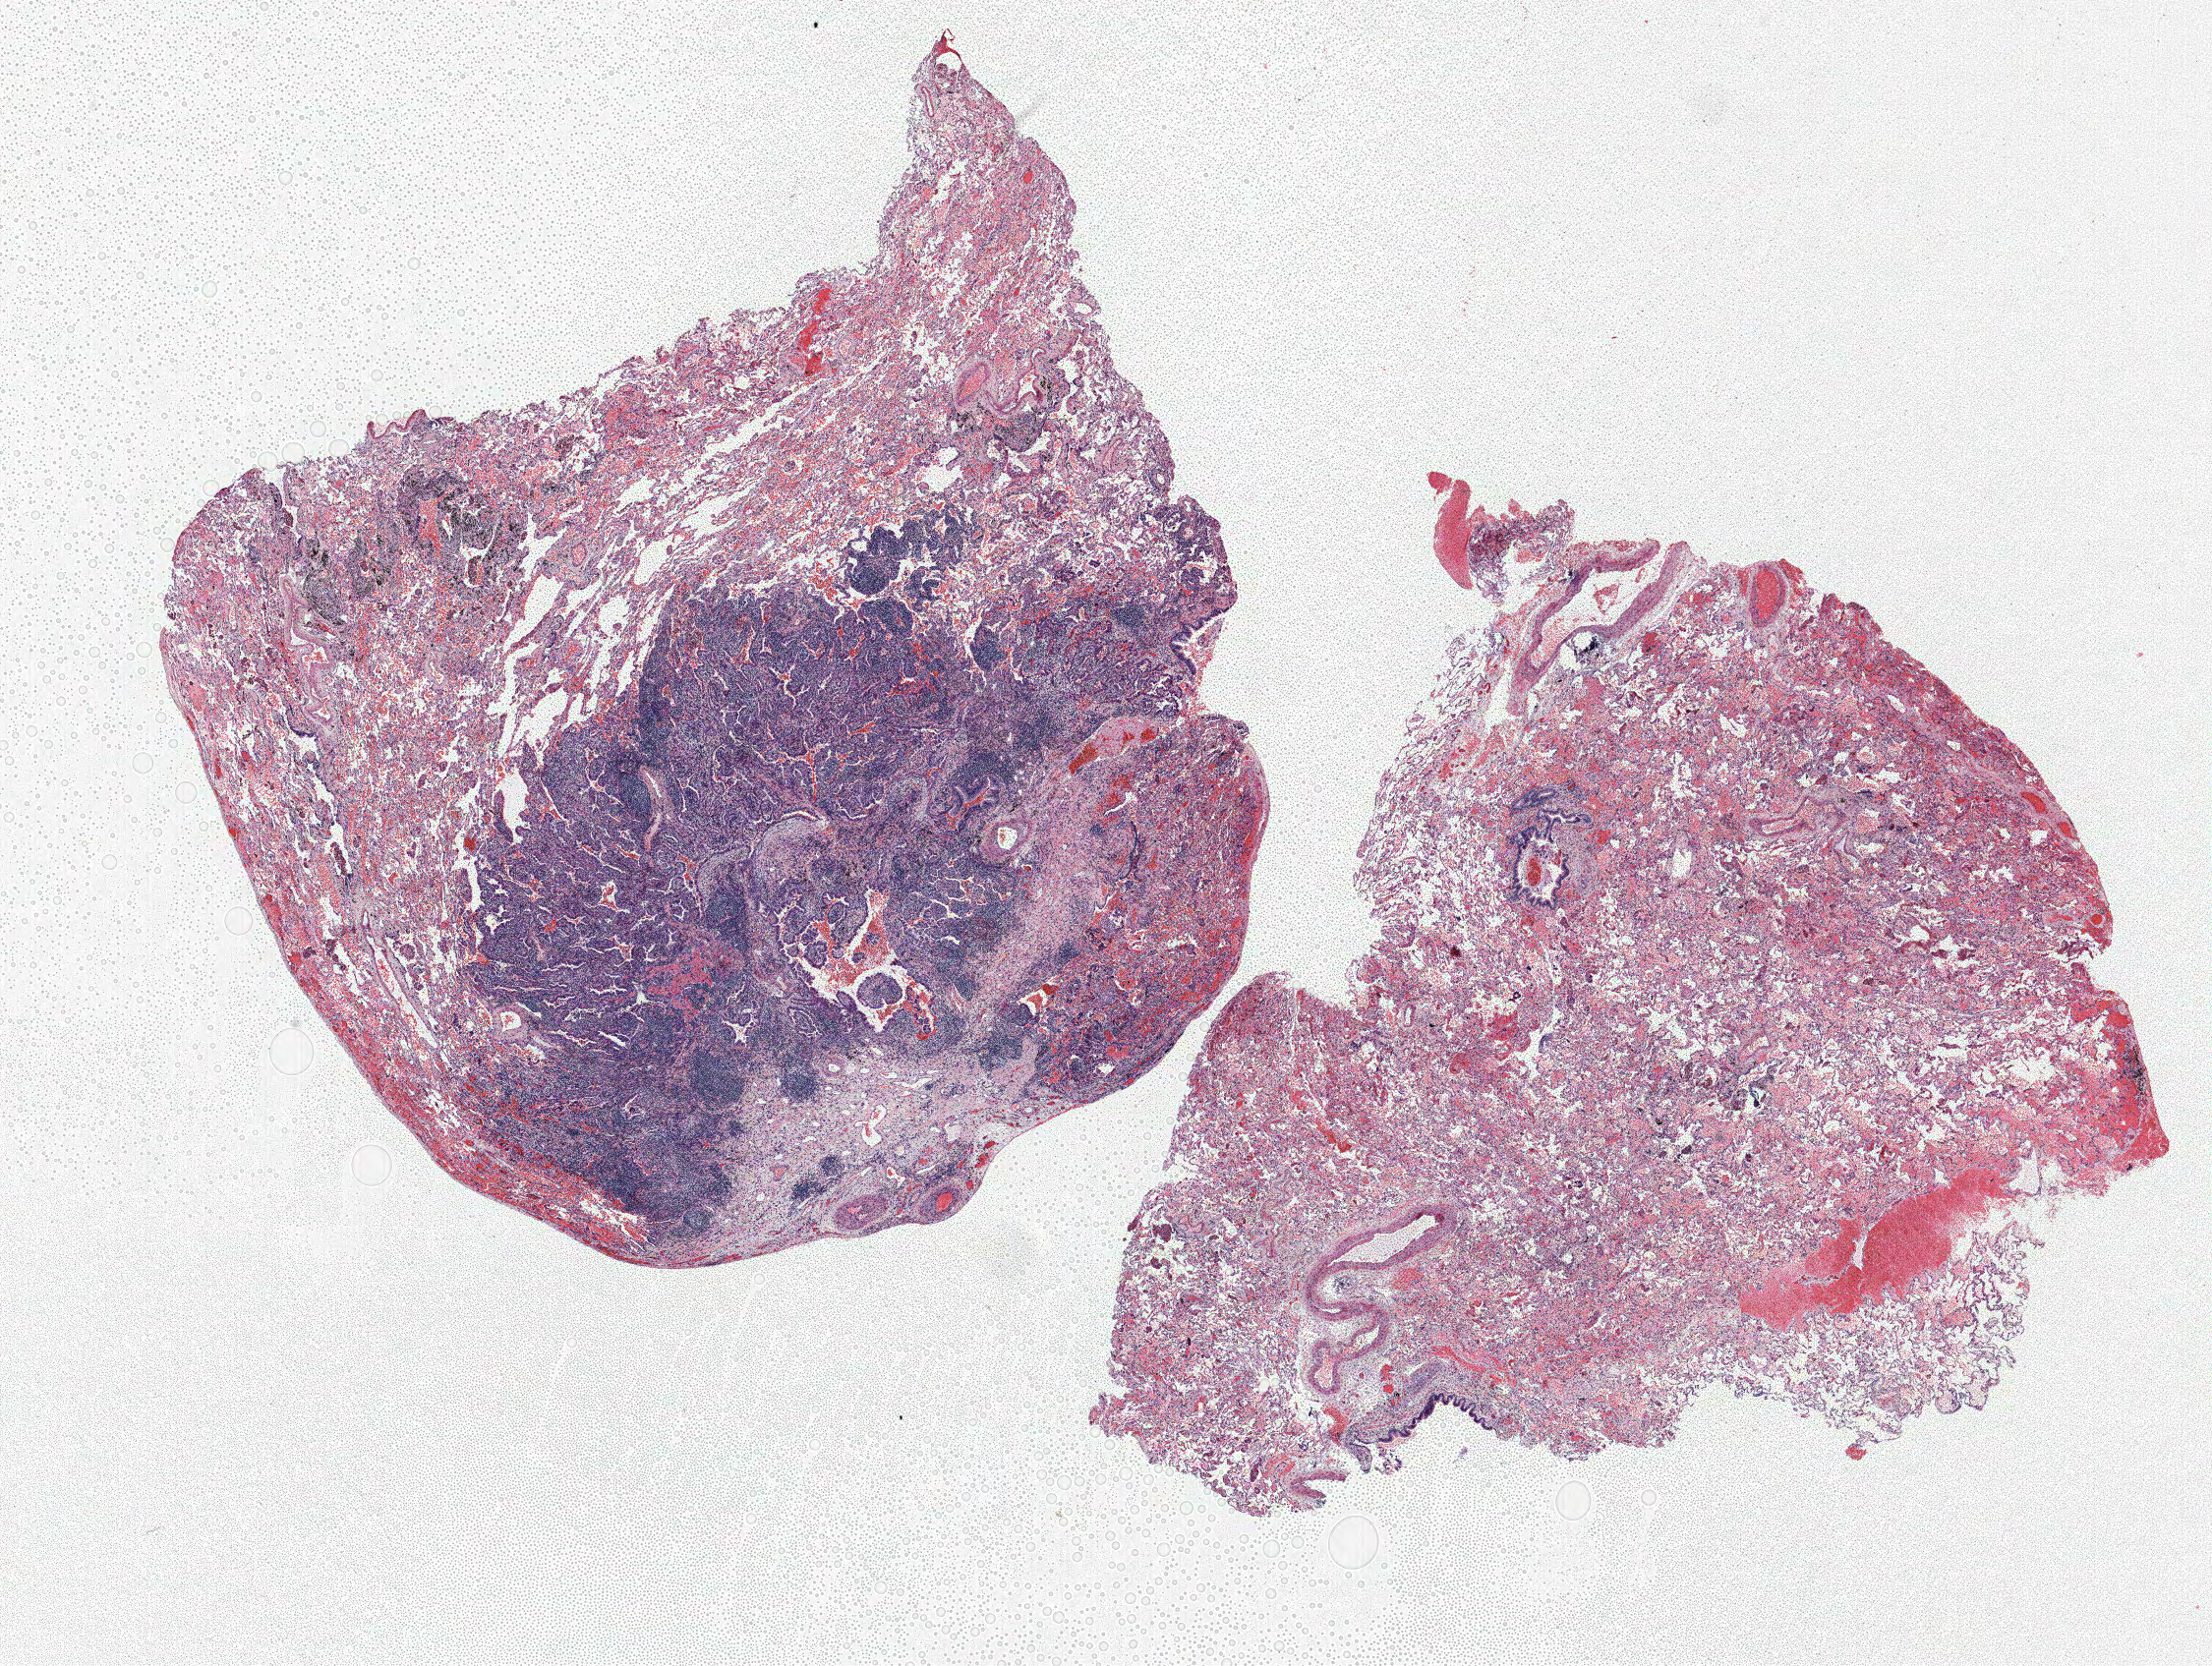
H&E-stained whole-slide image — whole scanned area (about 18.0 x 13.6 mm) shown as a low-resolution overview; formalin-fixed paraffin-embedded (FFPE) section; lung. Female, age 57 at enrolment. Current smoker at enrolment. Grade: moderately differentiated (G2).
* primary tumour location (clinical record): right lower lobe
* stage (AJCC 6th edition): IA
* tumour size (pathology): 8 mm
* participant's lung-cancer diagnosis: Adenocarcinoma, NOS